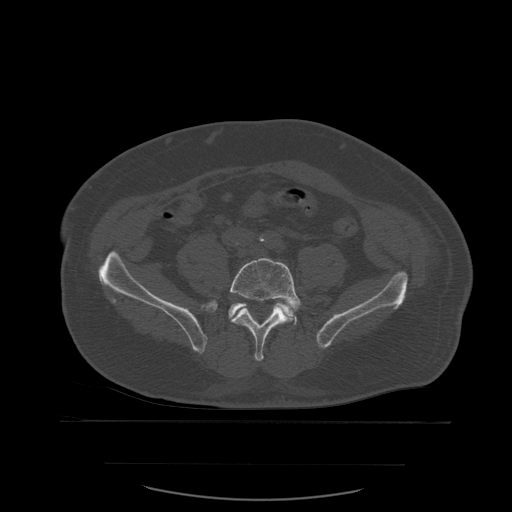
CT including the spine, one axial slice; slice 136 of 590 in the series (ordered by position); bone window (W 1800 / L 400 HU); 1.25 mm slice thickness; 512 × 512 image matrix. Patient age 71 years. Case-level facts recorded for this patient, not image findings: primary cancer: lung; vertebrae with lytic lesions (as recorded): T1, T2, L5, S1.
Structures marked on this image (semi-automatic segmentation, software-assisted and operator-edited):
- L5 vertebra: bounding box [x1, y1, x2, y2] px = [230, 258, 302, 362]